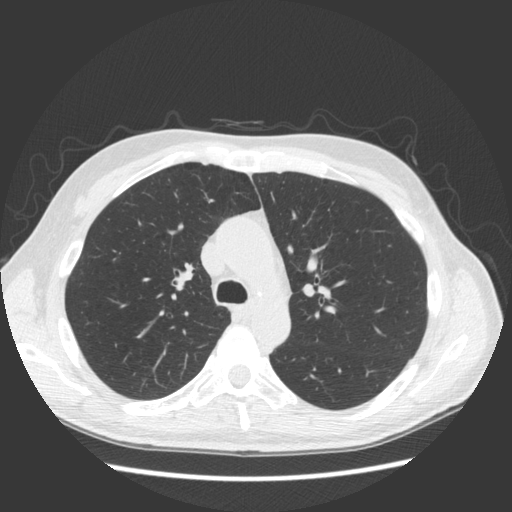
Chest CT (low-dose screening protocol), one axial image. Second annual screen. Lung window (W 1500 / L -600 HU). 2.5 mm slice thickness. 120 kVp. Male participant, aged 57 years at enrolment. Former smoker at enrolment.
Expert reader's lesion annotation, bounding box [x1, y1, x2, y2] px = [153, 251, 204, 299]. The screening reader recorded 3 non-calcified nodules or masses ≥4 mm on this exam (right middle lobe, right middle lobe, right middle lobe); which of them this box marks is not recorded. Participant outcome: lung cancer diagnosed 264 days after this screen — adenocarcinoma, NOS, right upper lobe, poorly differentiated (G3), stage IB (AJCC 6th edition), 25 mm at pathology.